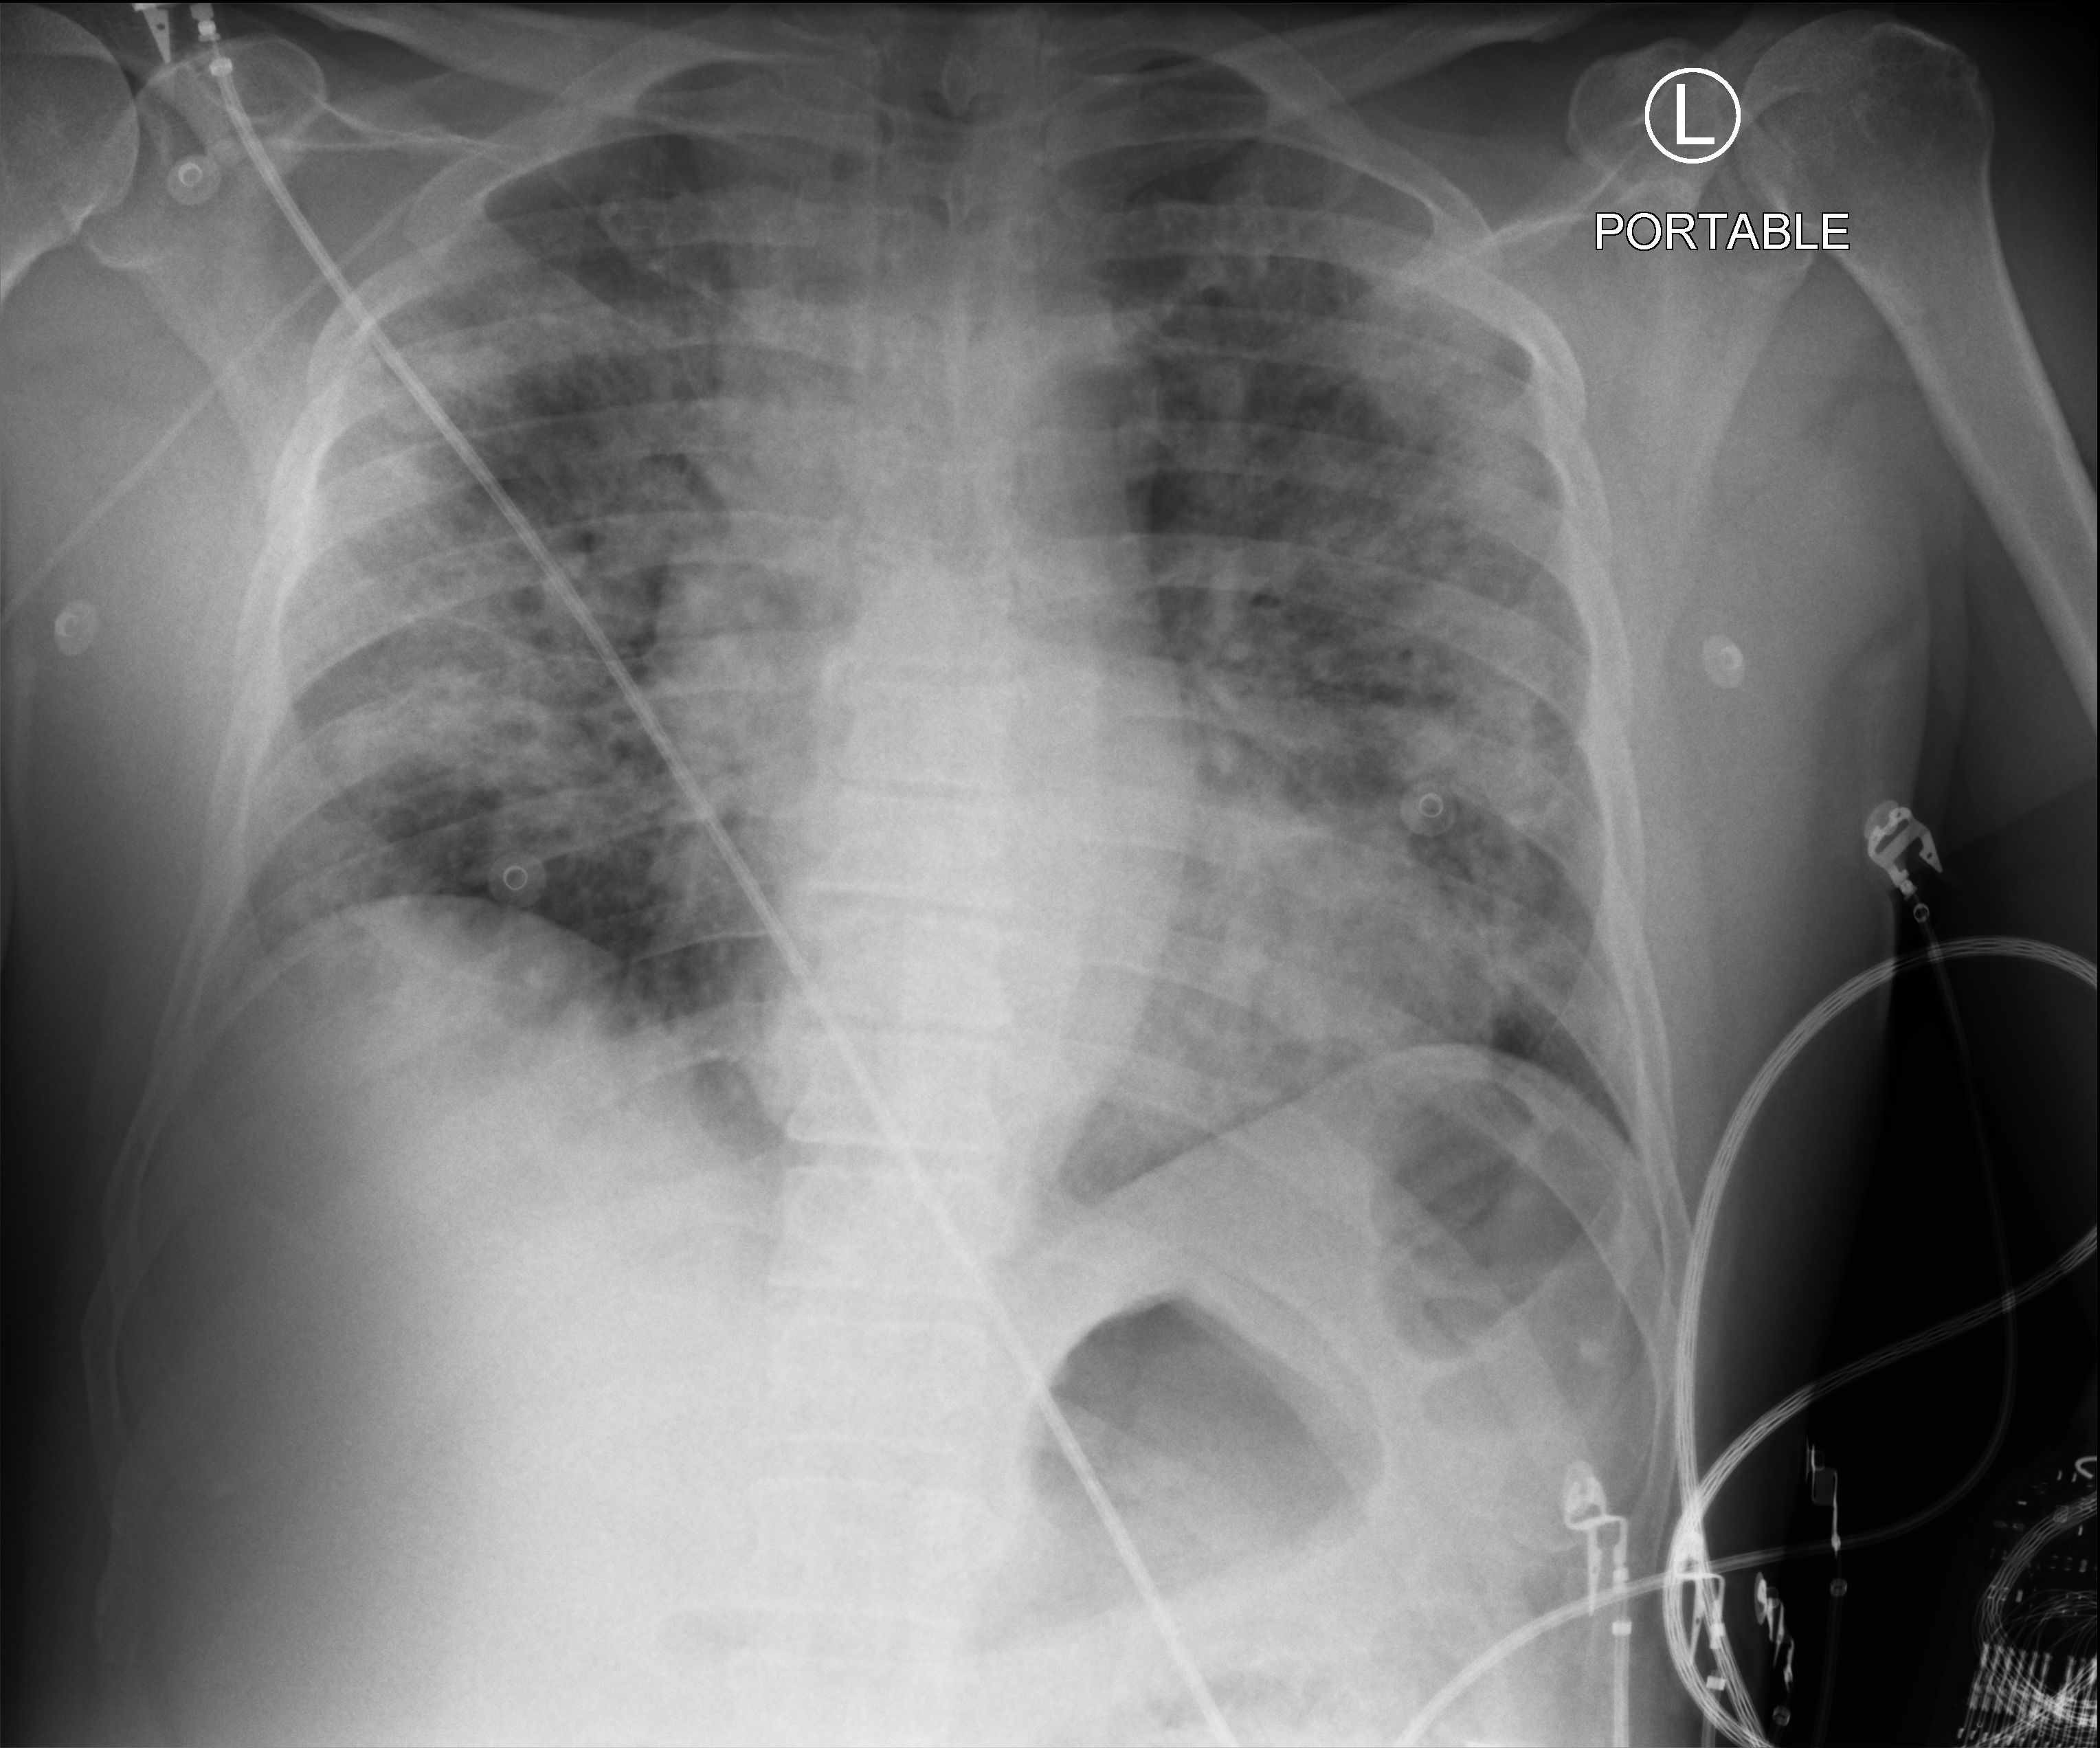
Chest X-ray (portable). Patient hospitalised with COVID-19; male, aged 60–74 years.
Hospital-stay facts (about this admission, not read from this image; timing relative to this image not recorded): mechanically ventilated during this hospital stay: no; hypertension (admission record): yes; other chronic lung disease (admission record): no.